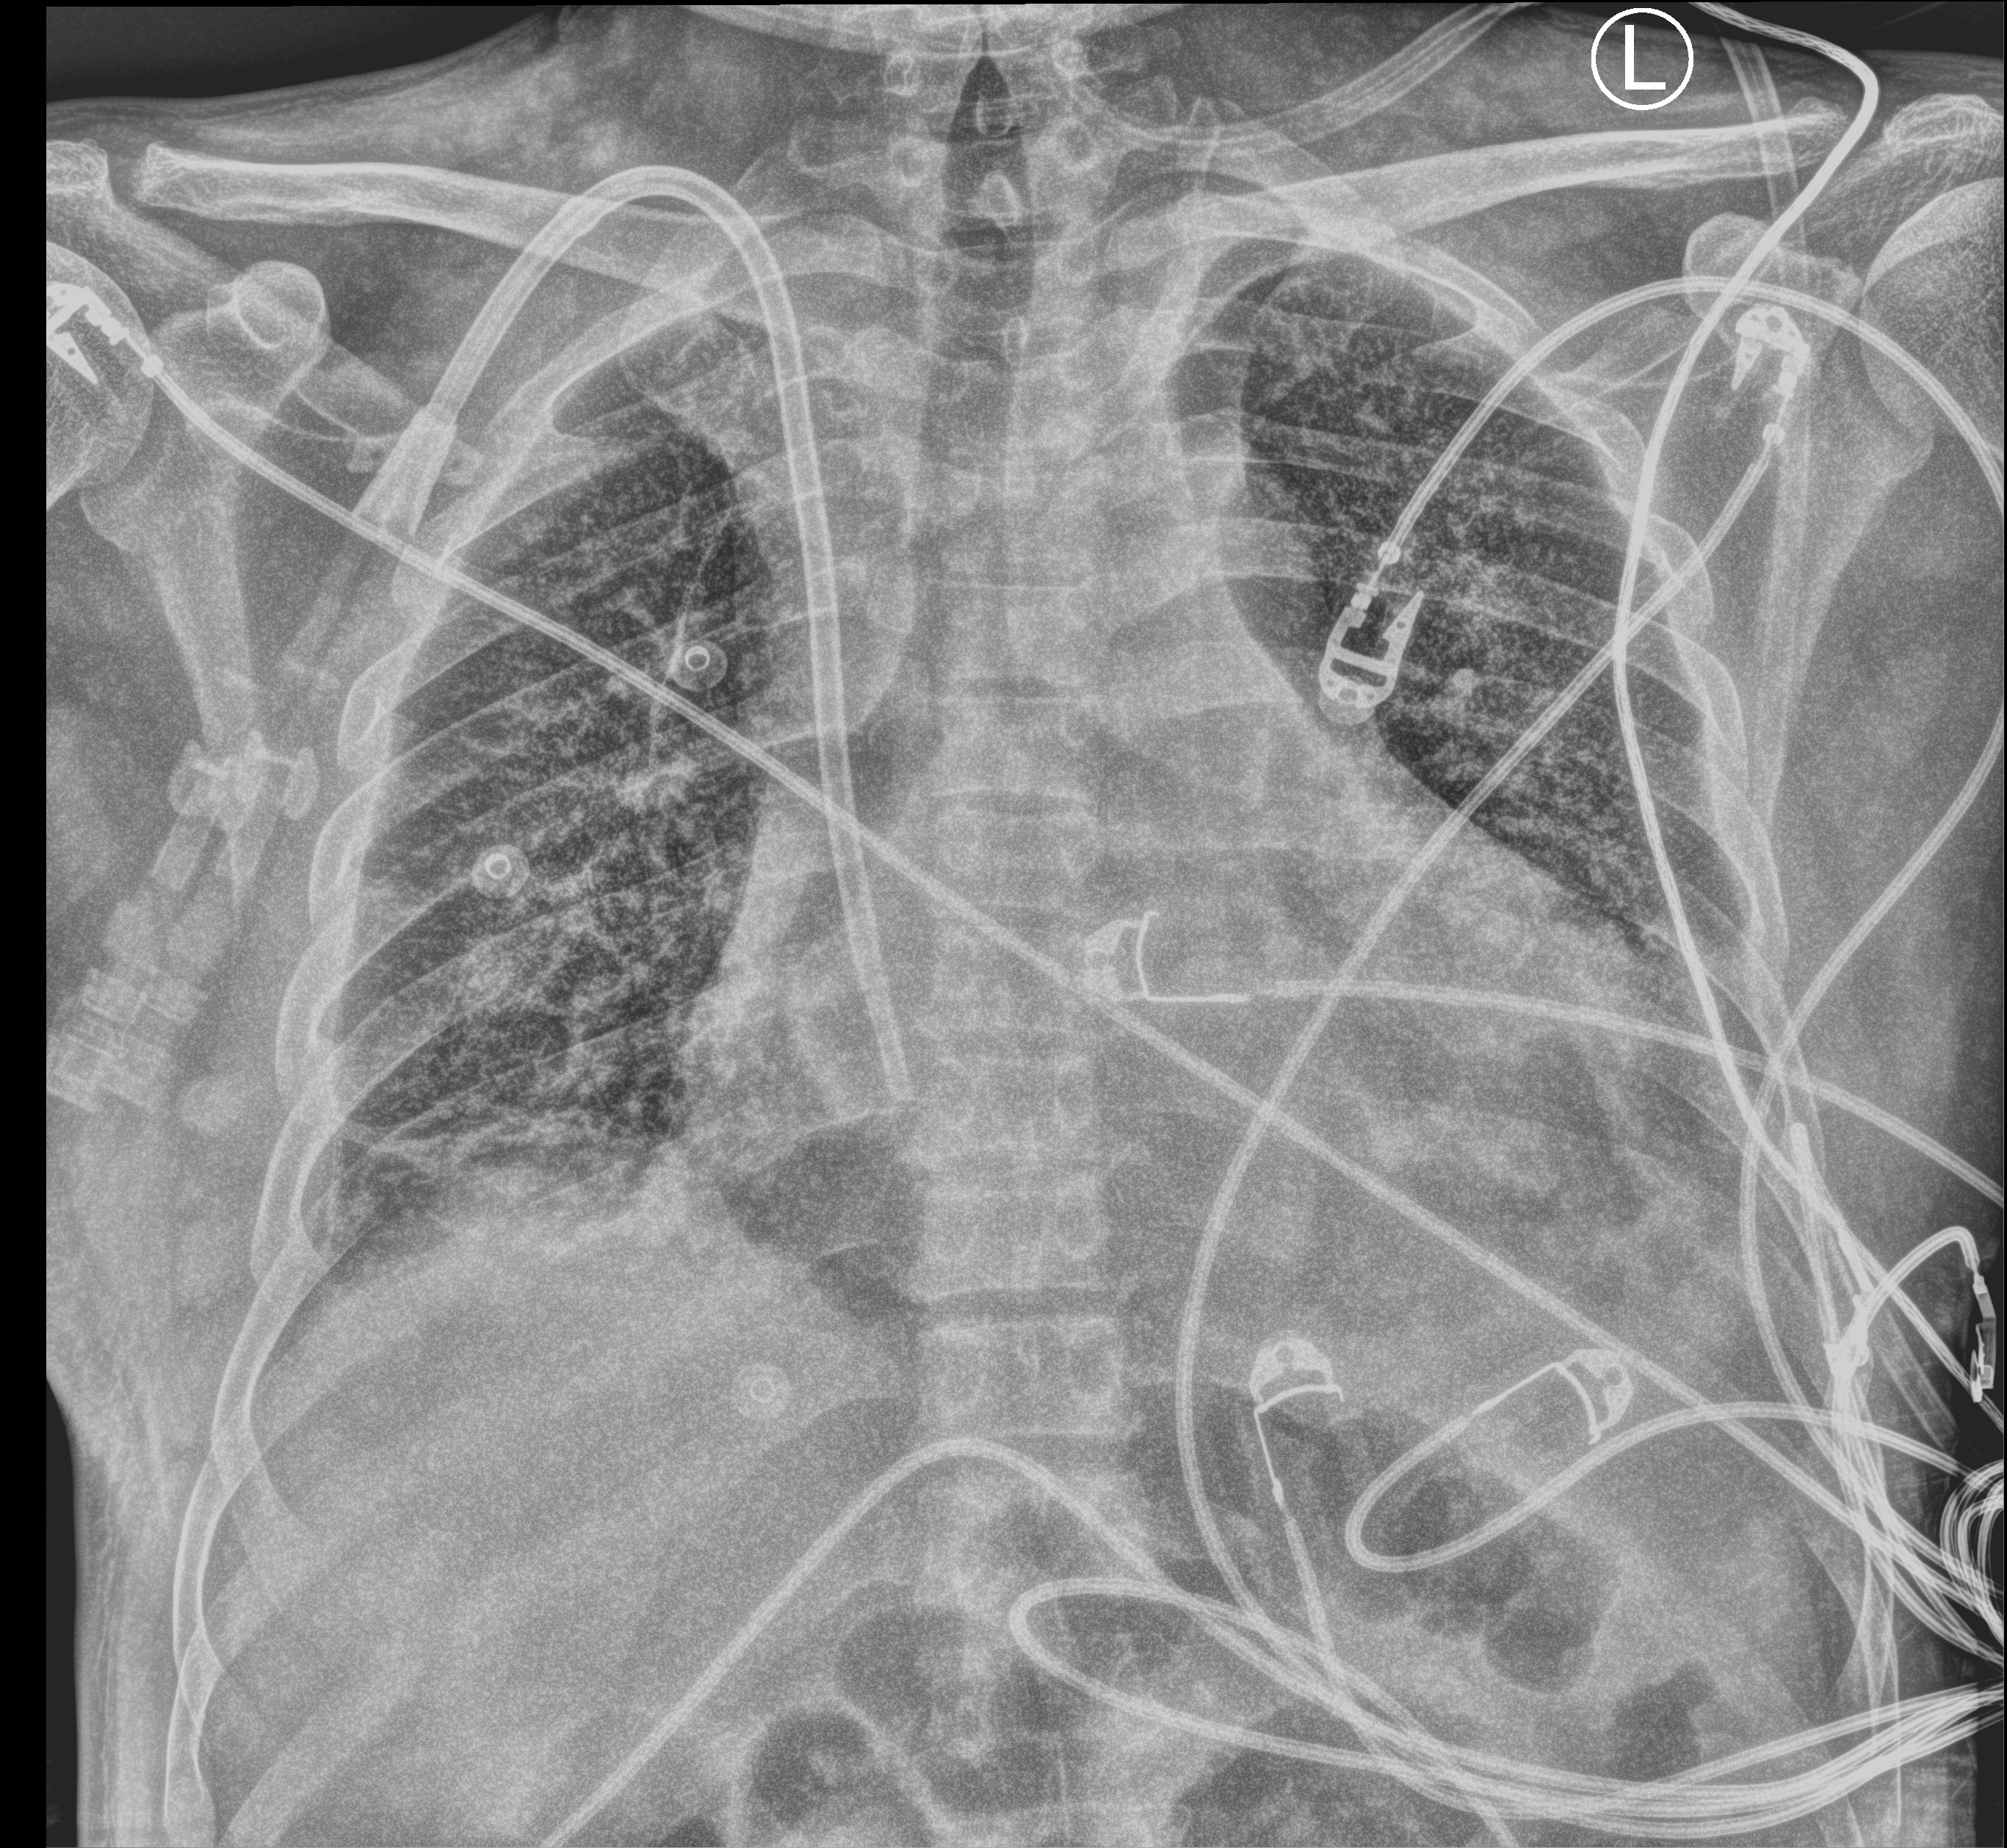
Bedside chest radiograph (computed radiography), anteroposterior (AP) projection. Patient hospitalised with COVID-19; male, aged 18–59 years.
Admission-level facts for this patient (not findings on this image; timing relative to this image not recorded):
- mechanically ventilated during this hospital stay: no
- admitted to intensive care during this hospital stay: no